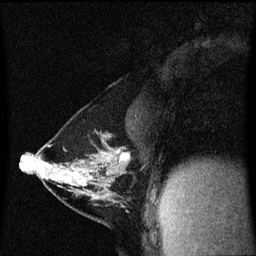
Breast MRI (dynamic contrast-enhanced), one sagittal slice; position 32 of 60 along the scan axis; dynamic contrast-enhanced series, image 2 of 3 at this slice position (ordered by acquisition); 1.5 T; TE 4.2 ms, TR 8.4 ms; 2 mm slice thickness; 256 × 256 image matrix, field of view 200 × 200 mm. Patient: female, 40 years. From the clinical record (not read from this slice): setting: breast cancer imaged before/during neoadjuvant chemotherapy; receptor status: triple-negative.
Annotated regions visible in this slice (semi-automatically segmented with operator editing):
- analysis volume of interest (the breast-tissue region the enhancement analysis was run in; not a lesion): bounding box <34,144,131,199> (left, top, right, bottom; pixels)
- tumour enhancement mask (voxels above the 70 % enhancement threshold inside the analysis volume of interest): <59,152,129,181>